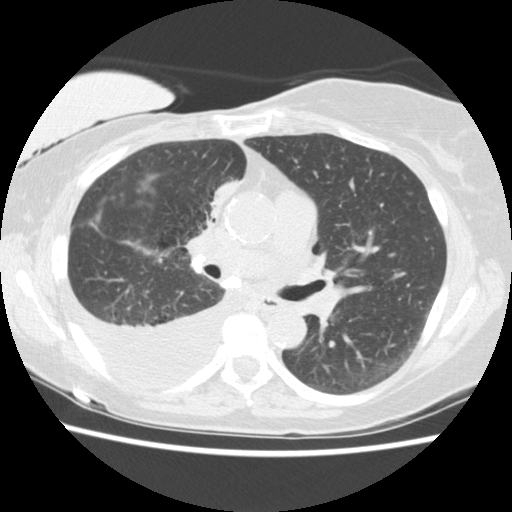
Low-dose screening chest CT, one axial slice. Slice 86 of 157 in the series (ordered by position). 120 kVp. Lung window (W 1500 / L -600 HU). 2.5 mm slice thickness. 512 × 512 image matrix, field of view 330 × 330 mm.
Structures marked on this image (manually delineated by an expert):
- lesion 1 (tumor, upper lobe of right lung): bounding box <210,180,240,217> (left, top, right, bottom; pixels)